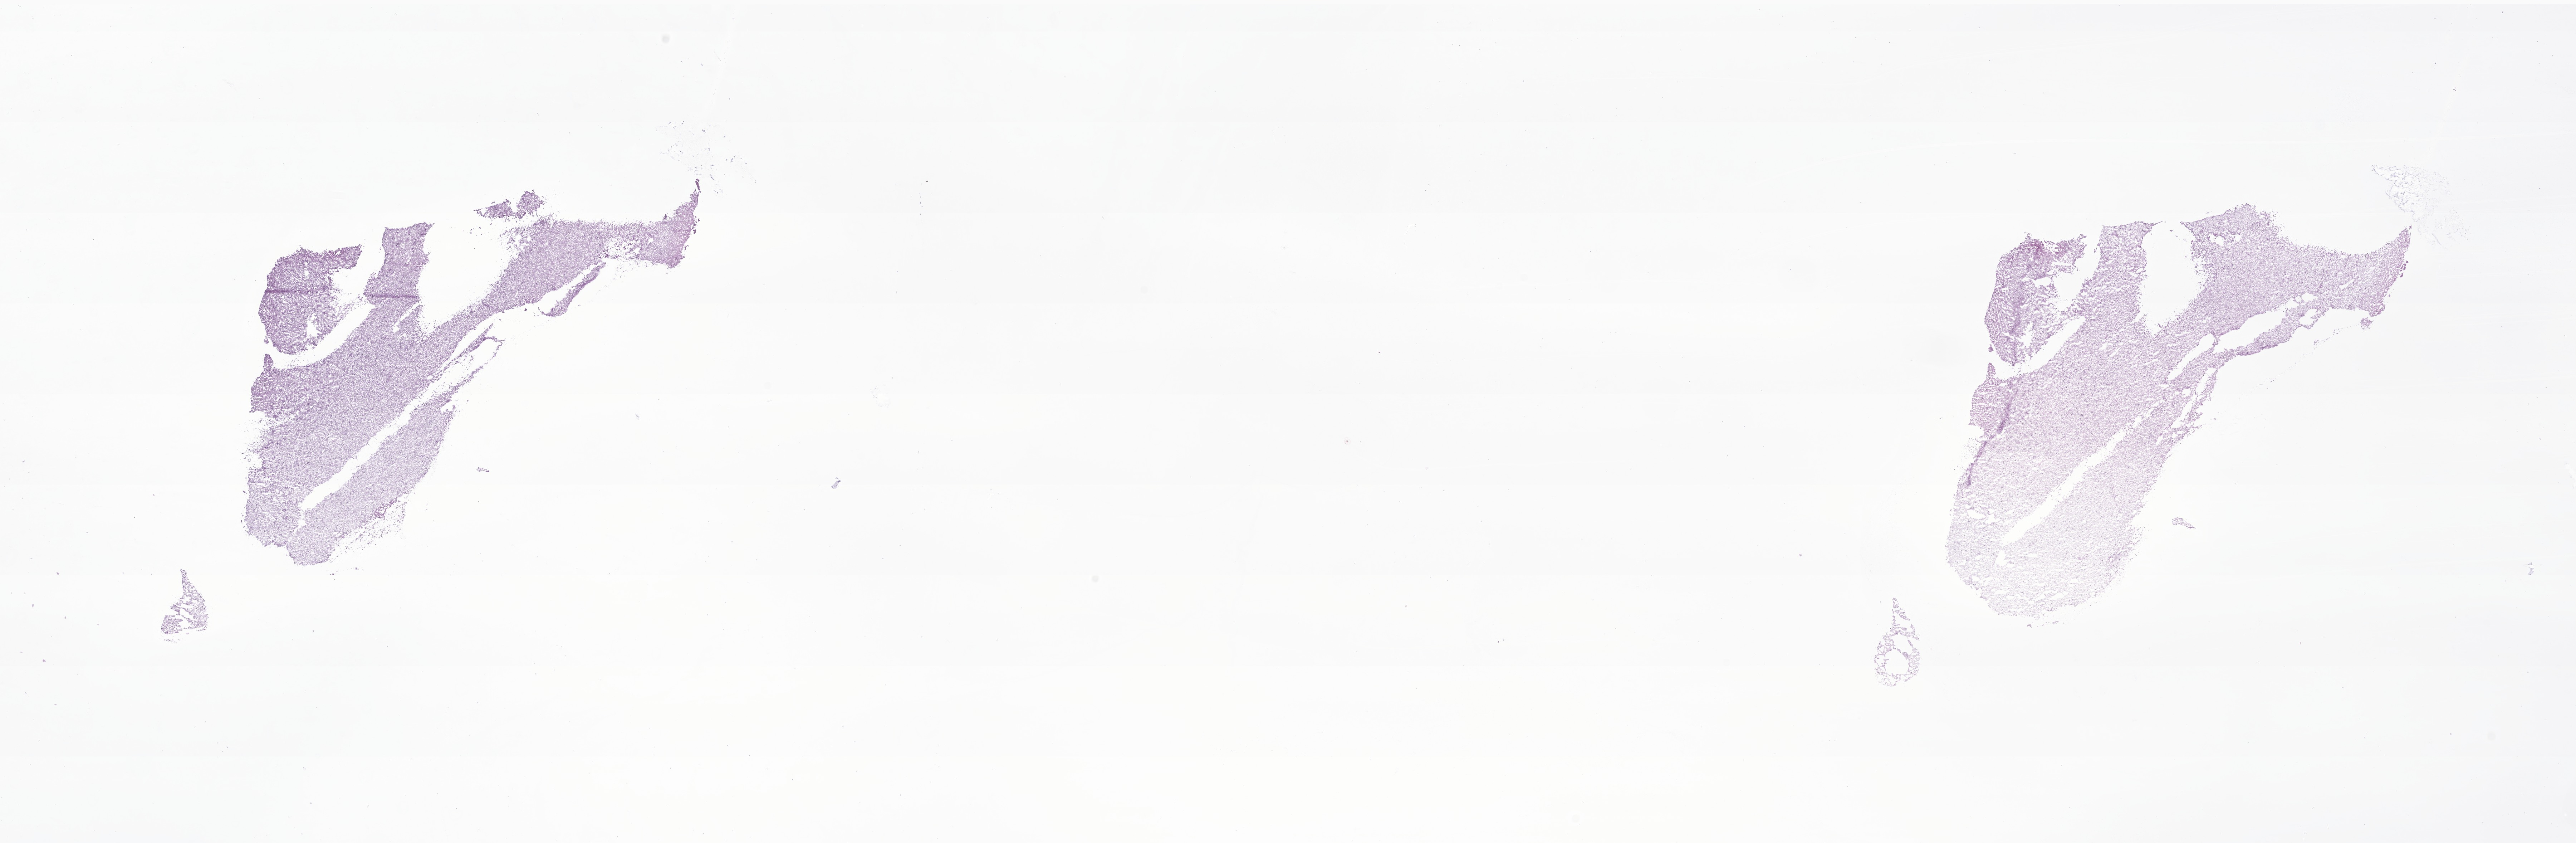
Haematoxylin and eosin whole-slide image of tumor tissue from the central nervous system, shown as a low-resolution overview of the whole scanned area (about 30.4 x 9.9 mm). Frozen section. Patient male; age 113 months (9 years 5 months).
- diagnosis: Glioma, malignant